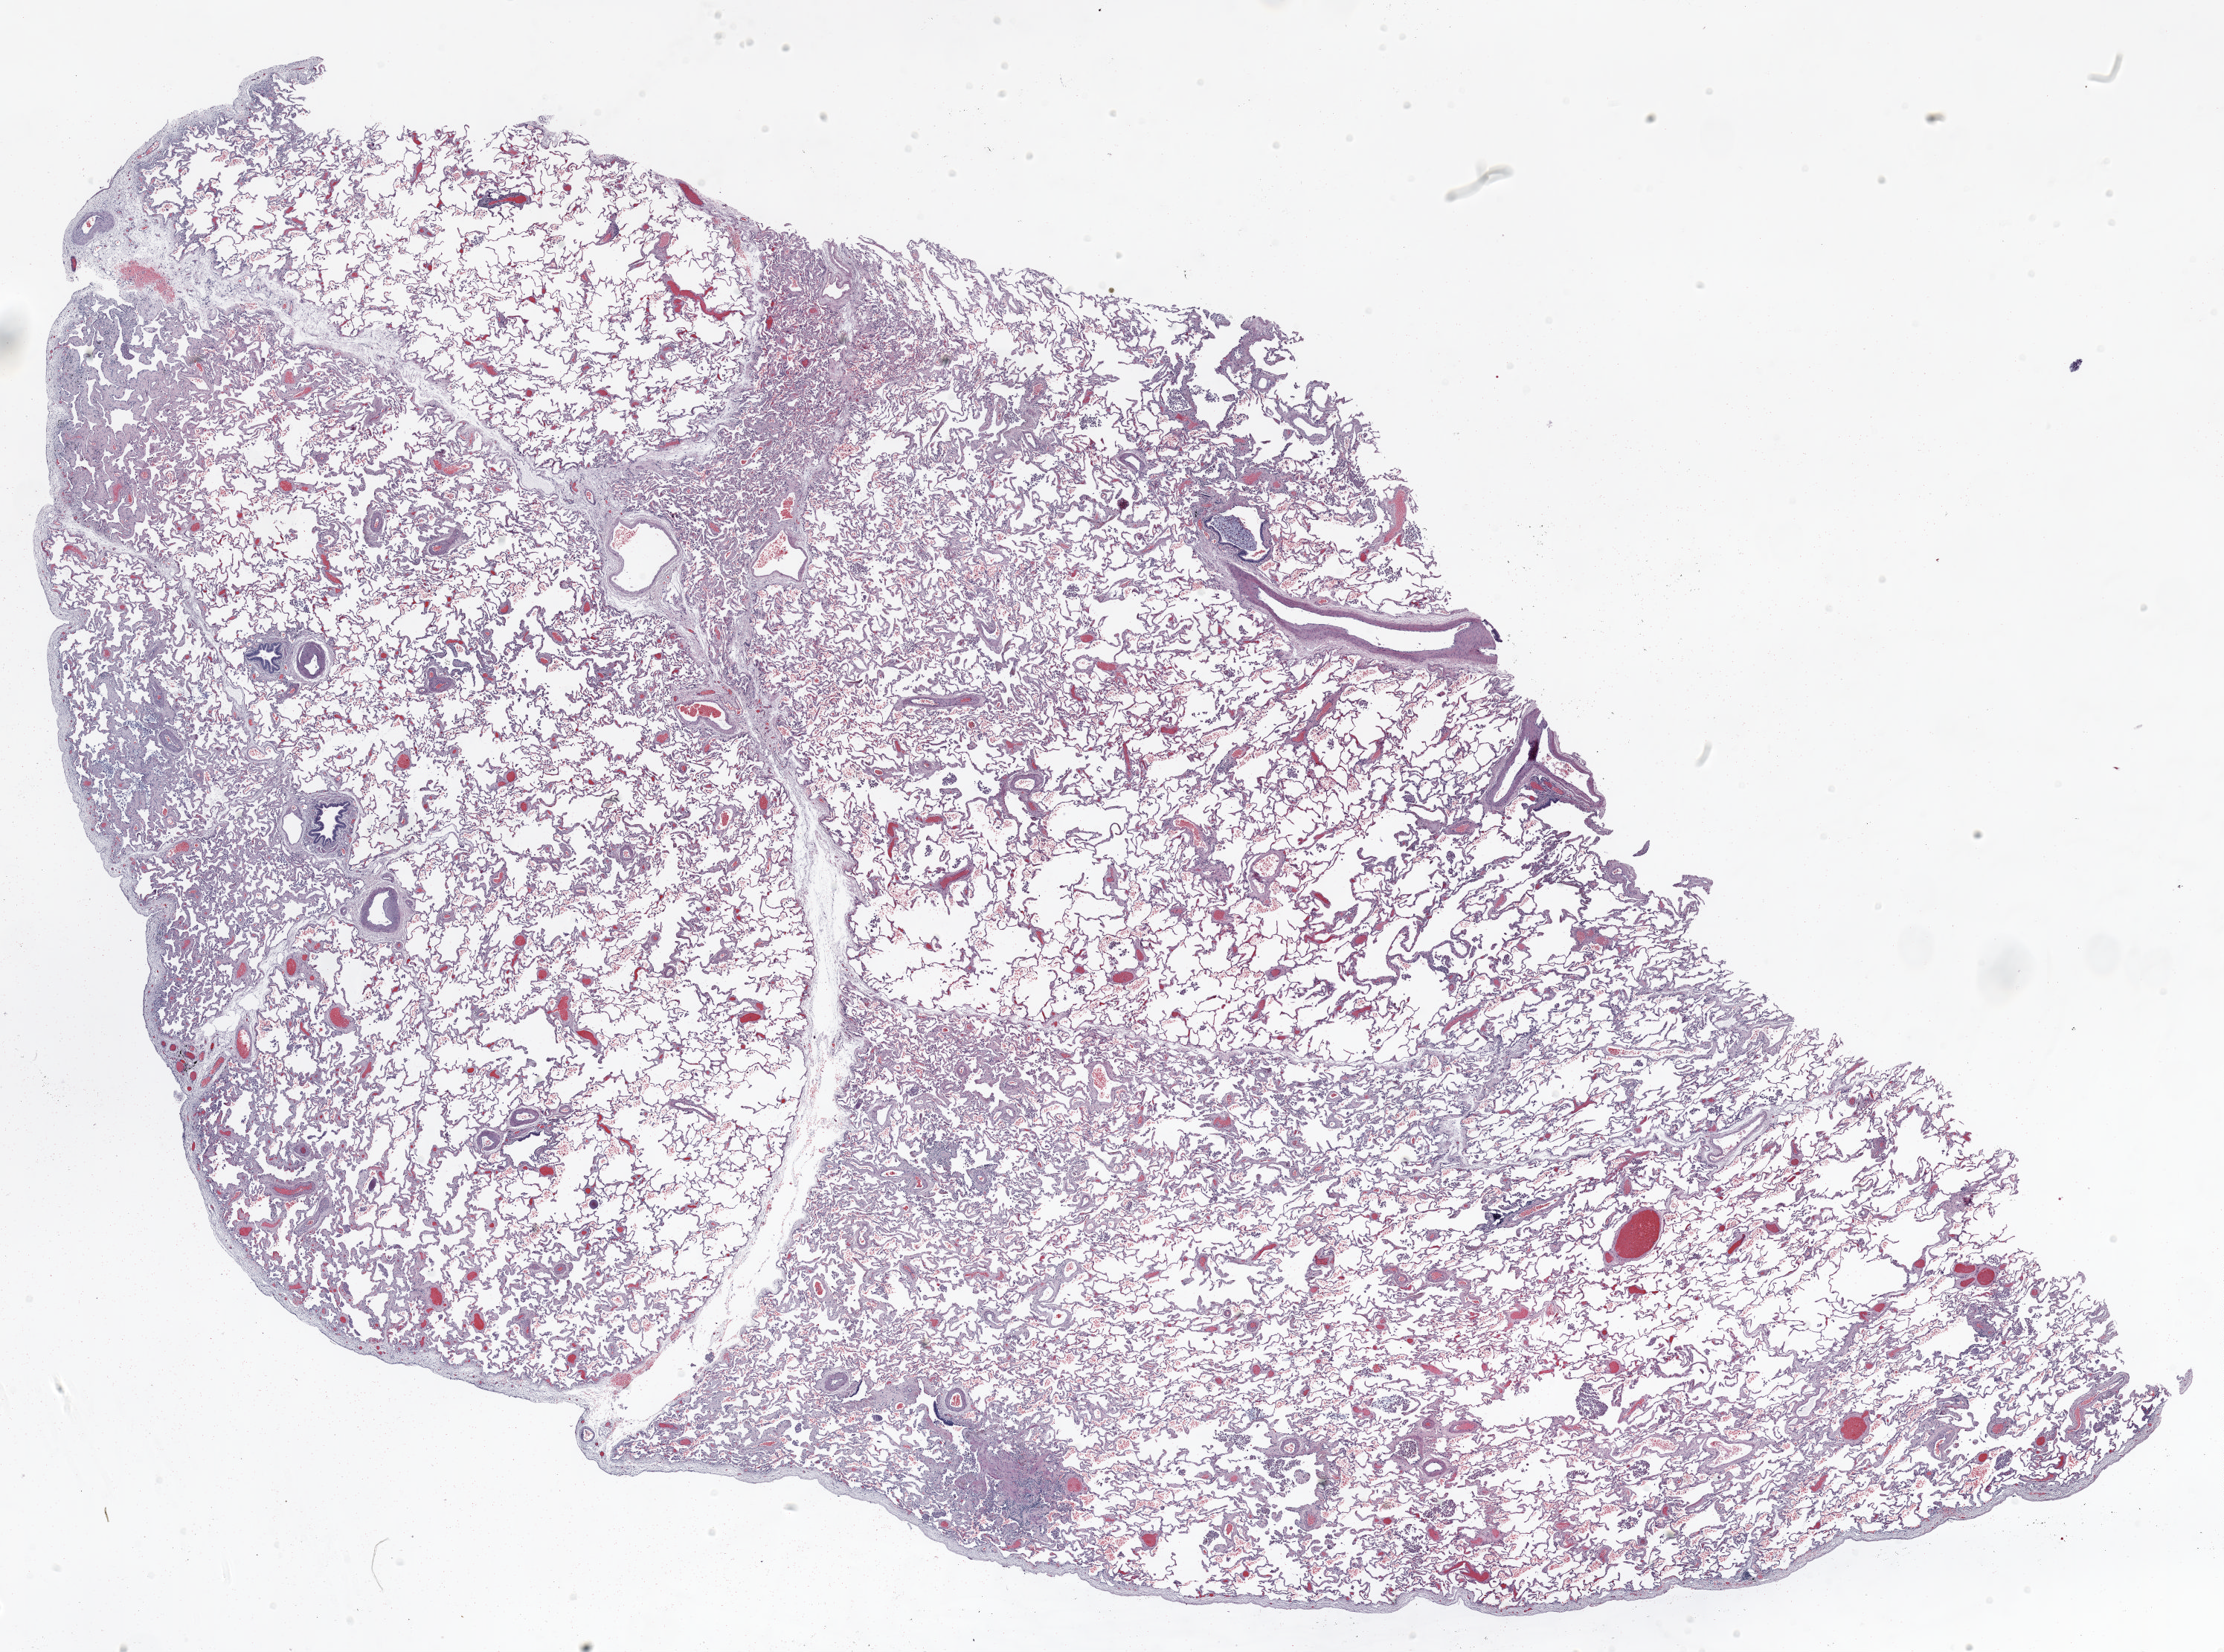
H&E-stained whole-slide image — a low-resolution overview of the entire scanned area, about 24.0 x 17.8 mm (acquisition: 20x scan), formalin-fixed paraffin-embedded (FFPE) section, lung. Male, age 68 at enrolment. Current smoker at enrolment. Grade: moderately differentiated (G2).
Primary tumour location (clinical record): right upper lobe. Participant's lung-cancer diagnosis: Adenocarcinoma, NOS (ICD-O-3 8140/3). Stage (AJCC 6th edition): IA. ICD-O-3 topography: upper lobe of lung (C34.1). Tumour size (pathology): 13 mm.